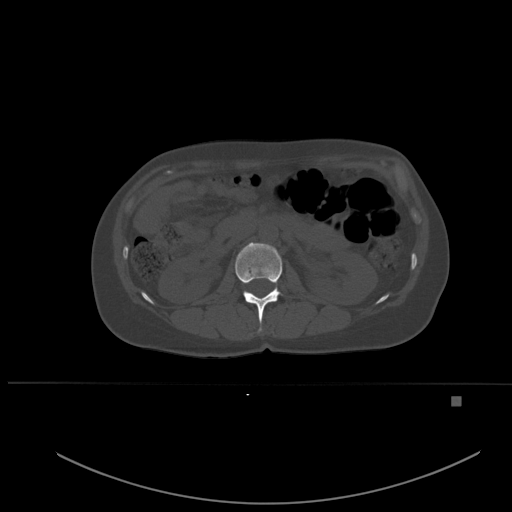
CT including the spine, one axial slice; bone window (W 1800 / L 400 HU); 1.5 mm slice thickness; 512 × 512 image matrix, field of view 443 × 443 mm. Patient: female, 49 years. From the clinical record (not read from this slice): primary cancer: breast; vertebrae with lytic lesions (as recorded): L3, T12, L4.
Structures marked on this image (semi-automatically segmented with operator editing):
- L1 vertebra: bounding box <235,242,282,332> (left, top, right, bottom; pixels)